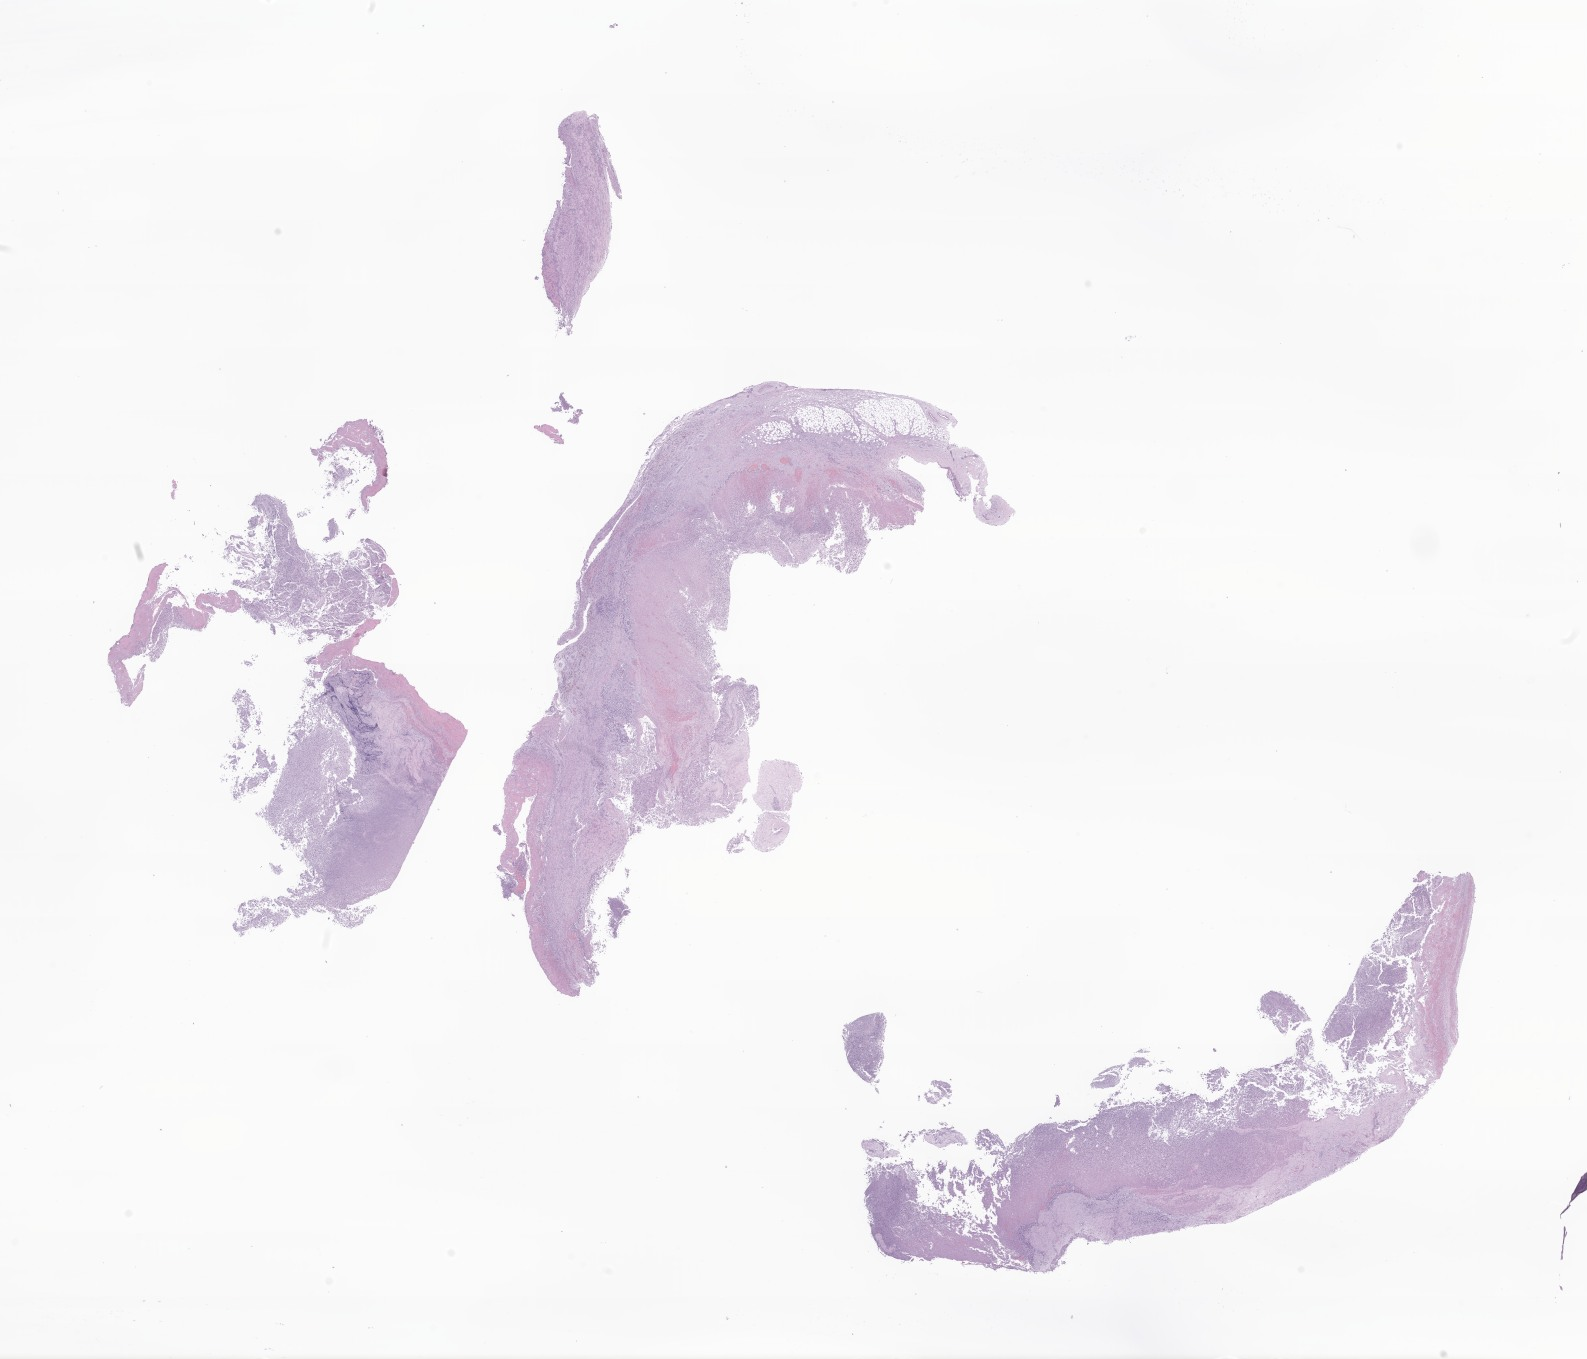
Whole-slide image, H&E stain of tumor tissue from the eye — whole scanned area (about 26.8 x 22.9 mm) shown as a low-resolution overview, formalin-fixed paraffin-embedded section. Female patient, age 191 months (15 years 11 months).
Diagnosis: Malignant melanoma, NOS.